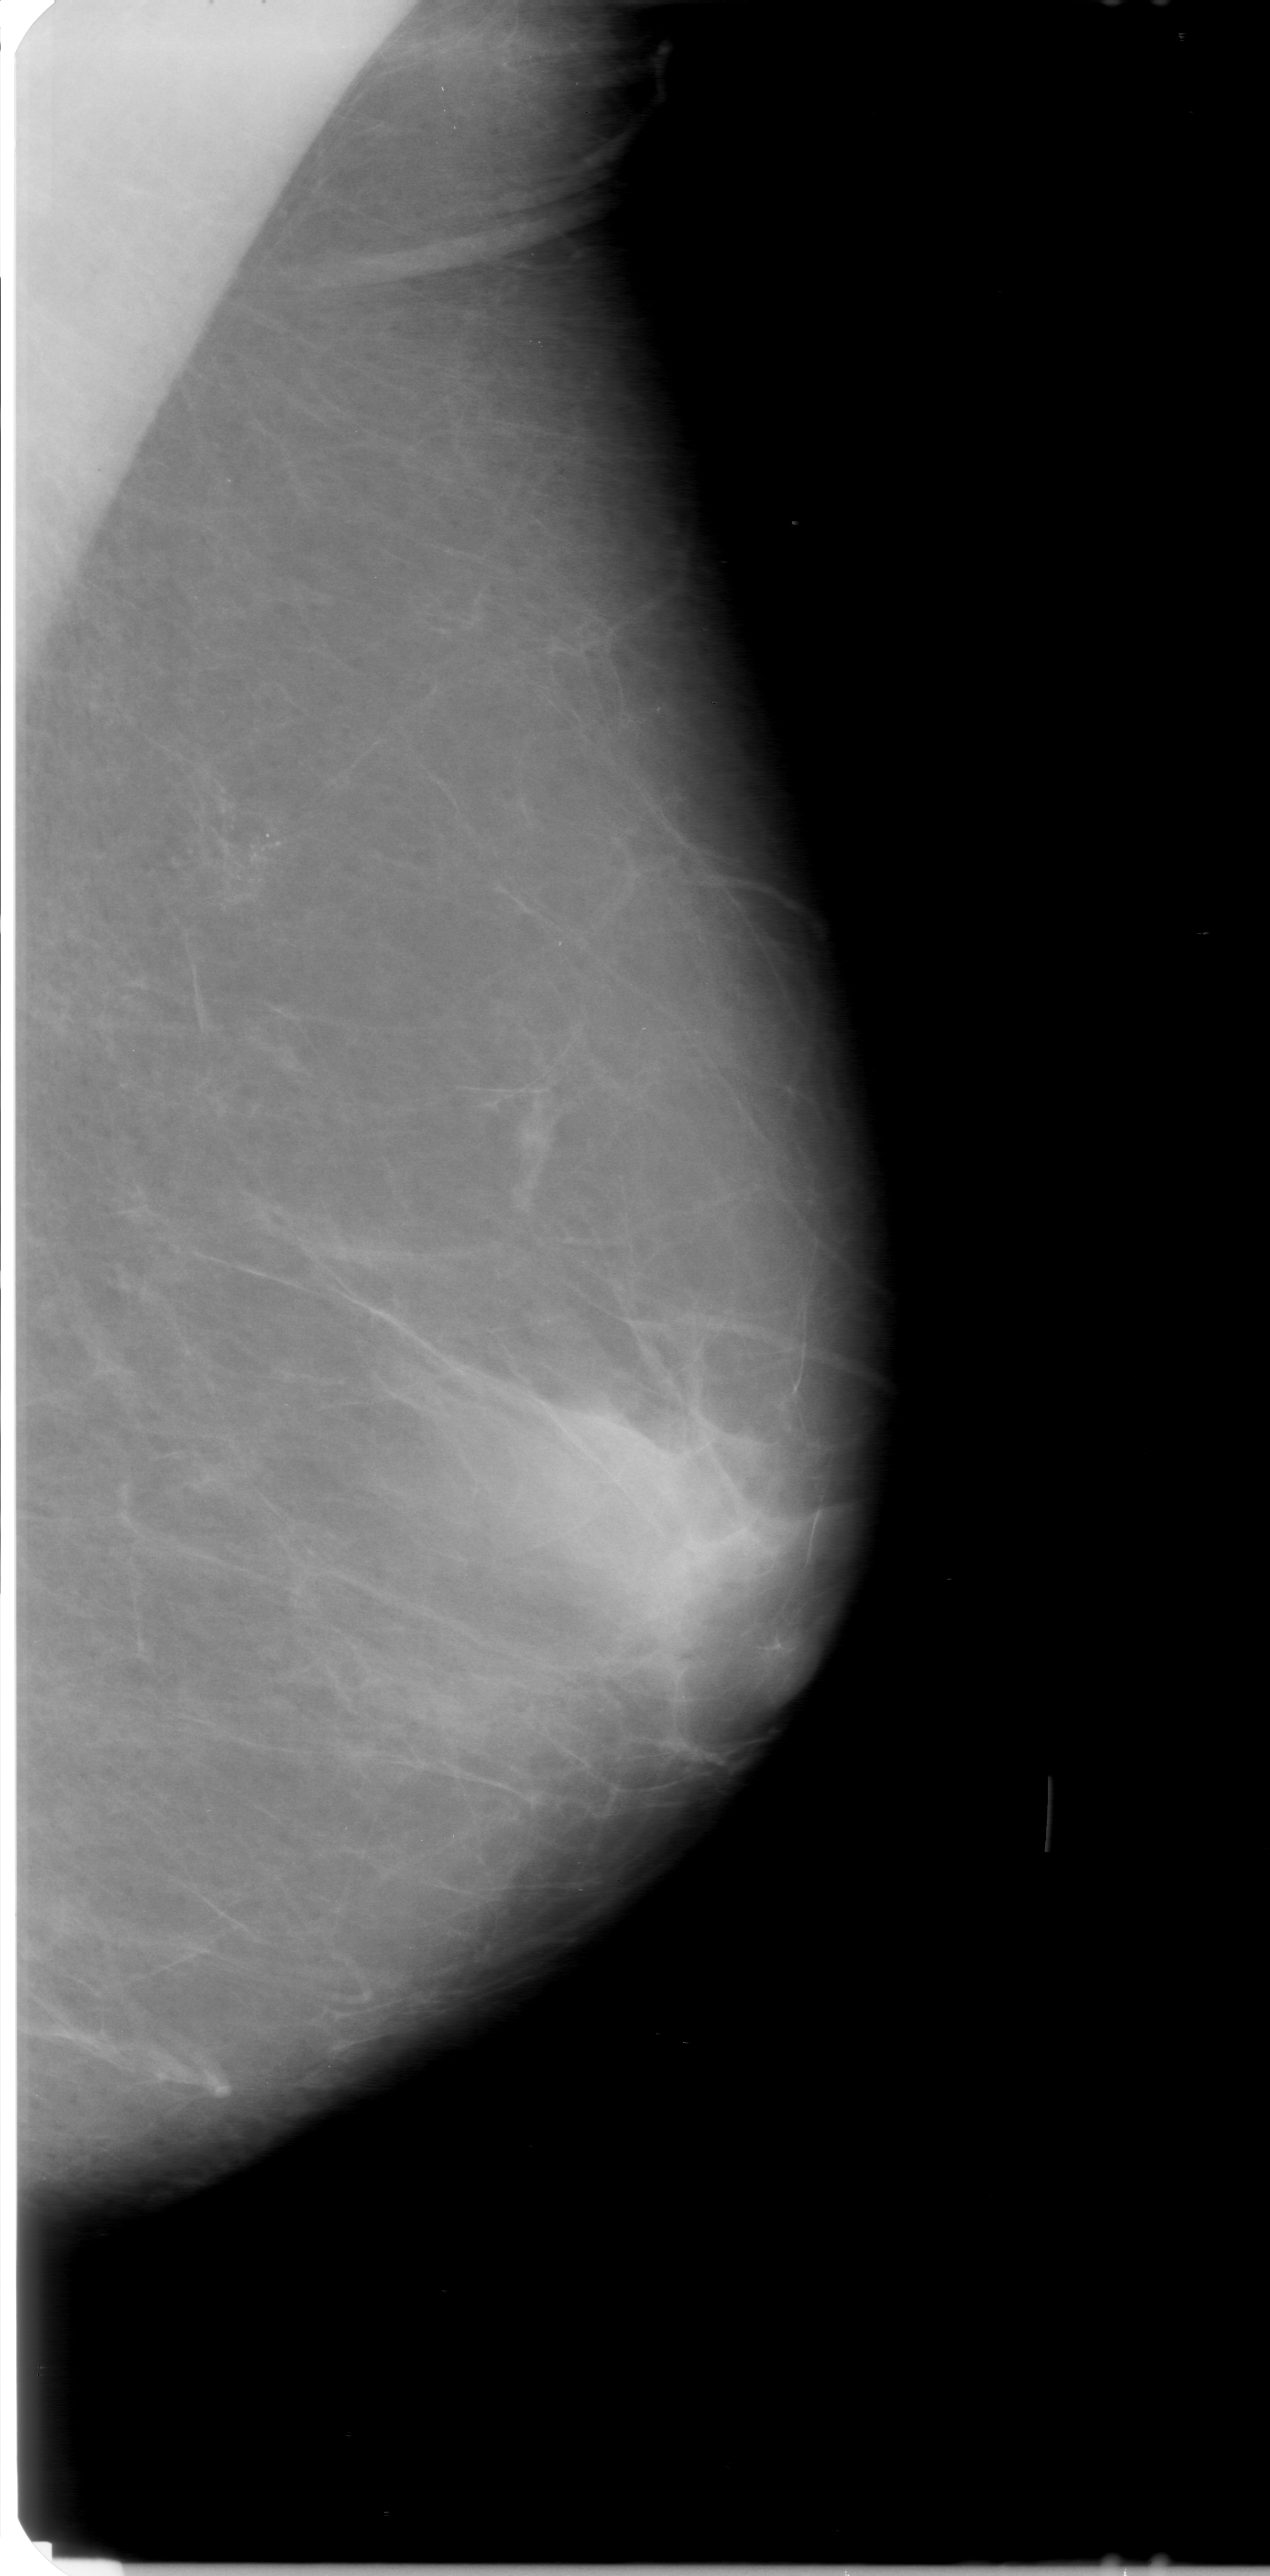
Scanned film-screen mammogram; left breast; mediolateral oblique (MLO) view; breast composition: almost entirely fatty (BI-RADS density category 1 of 4); 1270 × 2576 image matrix.
Expert-marked regions of interest on this image (one box per marked abnormality):
- calcifications, morphology fine linear branching, distribution clustered; BI-RADS assessment category 0 (incomplete: needs additional imaging); subtlety rating 4 on a 1 (subtle) to 5 (obvious) scale; pathology (as recorded): malignant: bounding box (x1, y1, x2, y2) in pixels: (90, 716, 388, 1016)